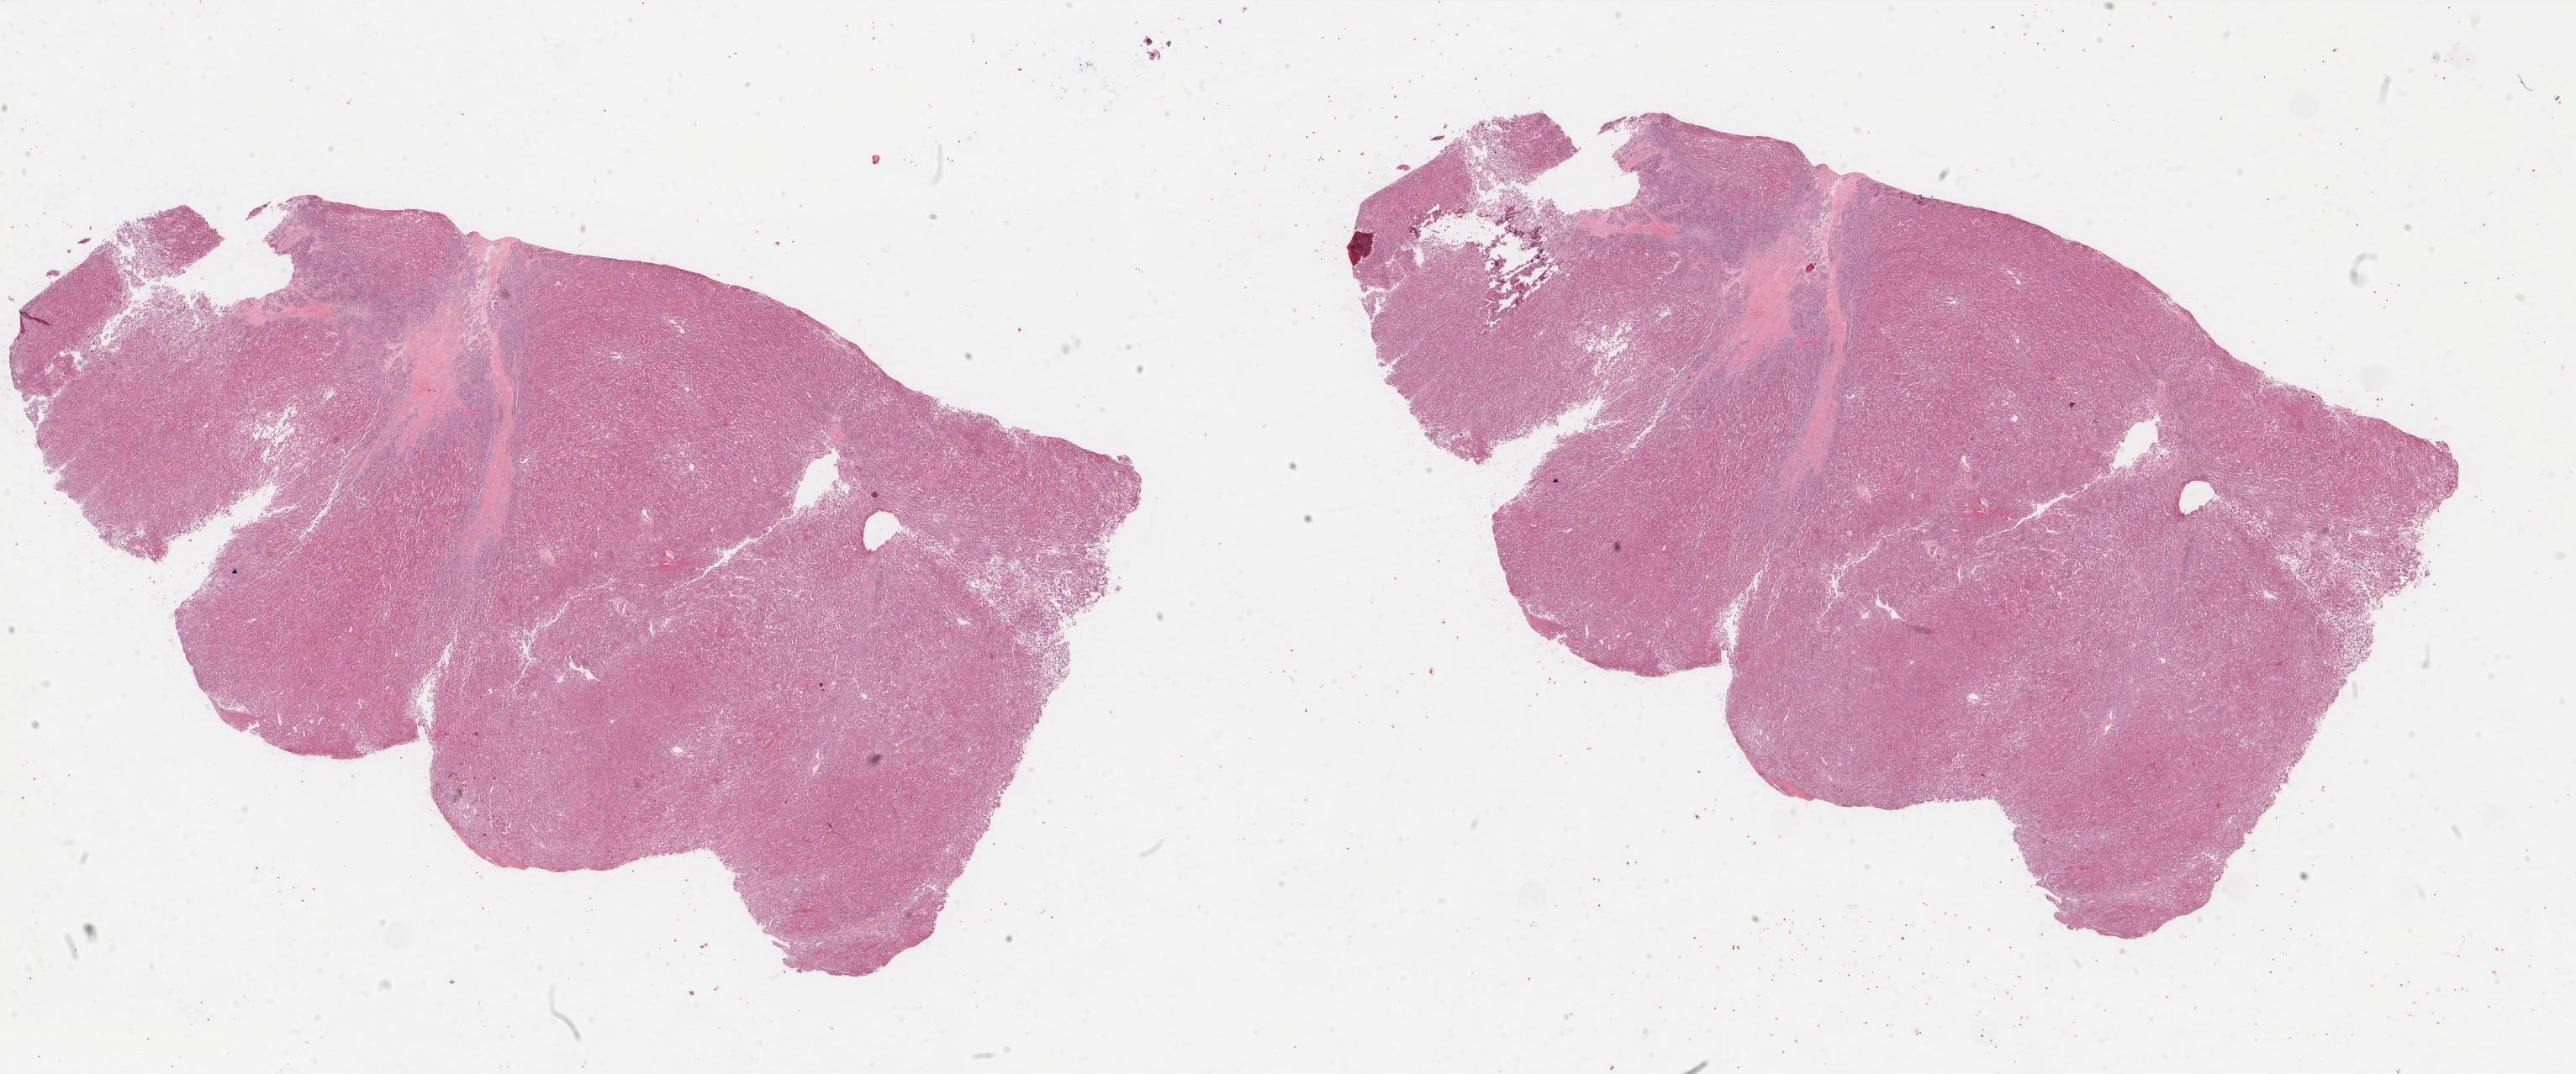
Hematoxylin and eosin (H&E) stained whole-slide image — a low-resolution overview of the entire scanned area, about 48.5 x 20.2 mm (from a 40x scan), formalin-fixed paraffin-embedded (FFPE) diagnostic section, primary tumour sample from the kidney. Male patient; age at initial diagnosis 44 years.
AJCC pathologic stage: I. Pathologic diagnosis: Renal cell carcinoma, chromophobe type. TNM: T1a NX.